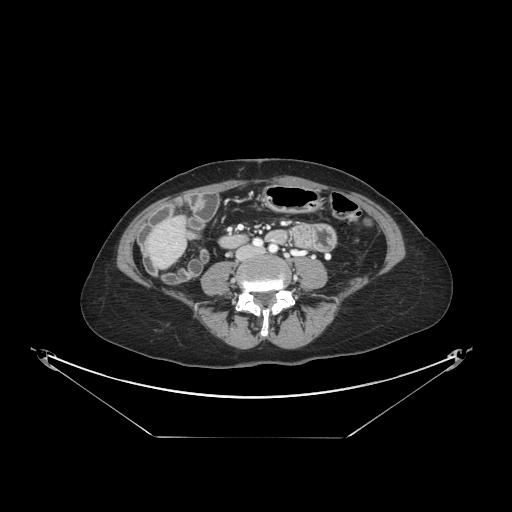
Contrast-enhanced abdominal CT, one axial slice. Slice 23 of 148 in the series (ordered by position). Reconstruction kernel STANDARD. 120 kVp. Intravenous contrast given. Soft-tissue window (W 400 / L 40 HU). 2.5 mm slice thickness. 512 × 512 image matrix, field of view 500 × 500 mm. Female patient, age 73 years. Case-level facts recorded for this patient, not image findings: diagnosis: colorectal cancer liver metastases, imaged before liver resection; multiple liver metastases: no; largest metastasis: 1 cm; disease in both lobes: no.
Outlined on this slice (manually delineated by an expert):
- liver: box from (x=152, y=219) to (x=185, y=265) px
- planned liver remnant (the part of the liver to remain after resection): (x=170, y=219)–(x=183, y=231)